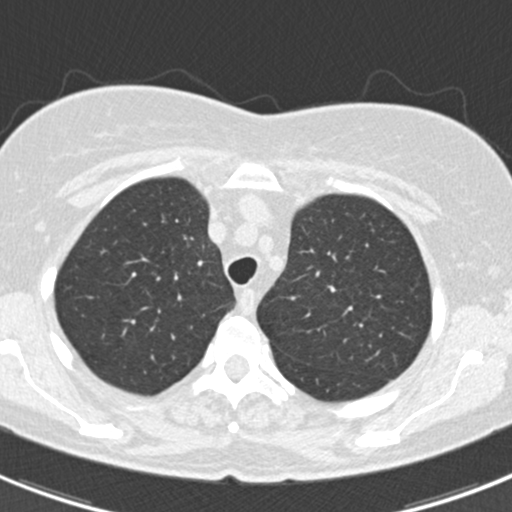
Chest CT (low-dose screening protocol), one axial image. Baseline annual screen. Lung window (W 1500 / L -600 HU). 120 kVp. Slice 45 of 184 in the series. Female participant, aged 60 years at enrolment. Current smoker at enrolment.
Lesion marked by an expert reader, box from (x=386, y=304) to (x=426, y=341) px. The screening reader recorded 3 non-calcified nodules or masses ≥4 mm on this exam; which of them this box marks is not recorded. Official screen result: positive, change unspecified: nodule(s) >= 4 mm or enlarging nodule(s), mass(es), or other non-specific abnormalities suspicious for lung cancer.